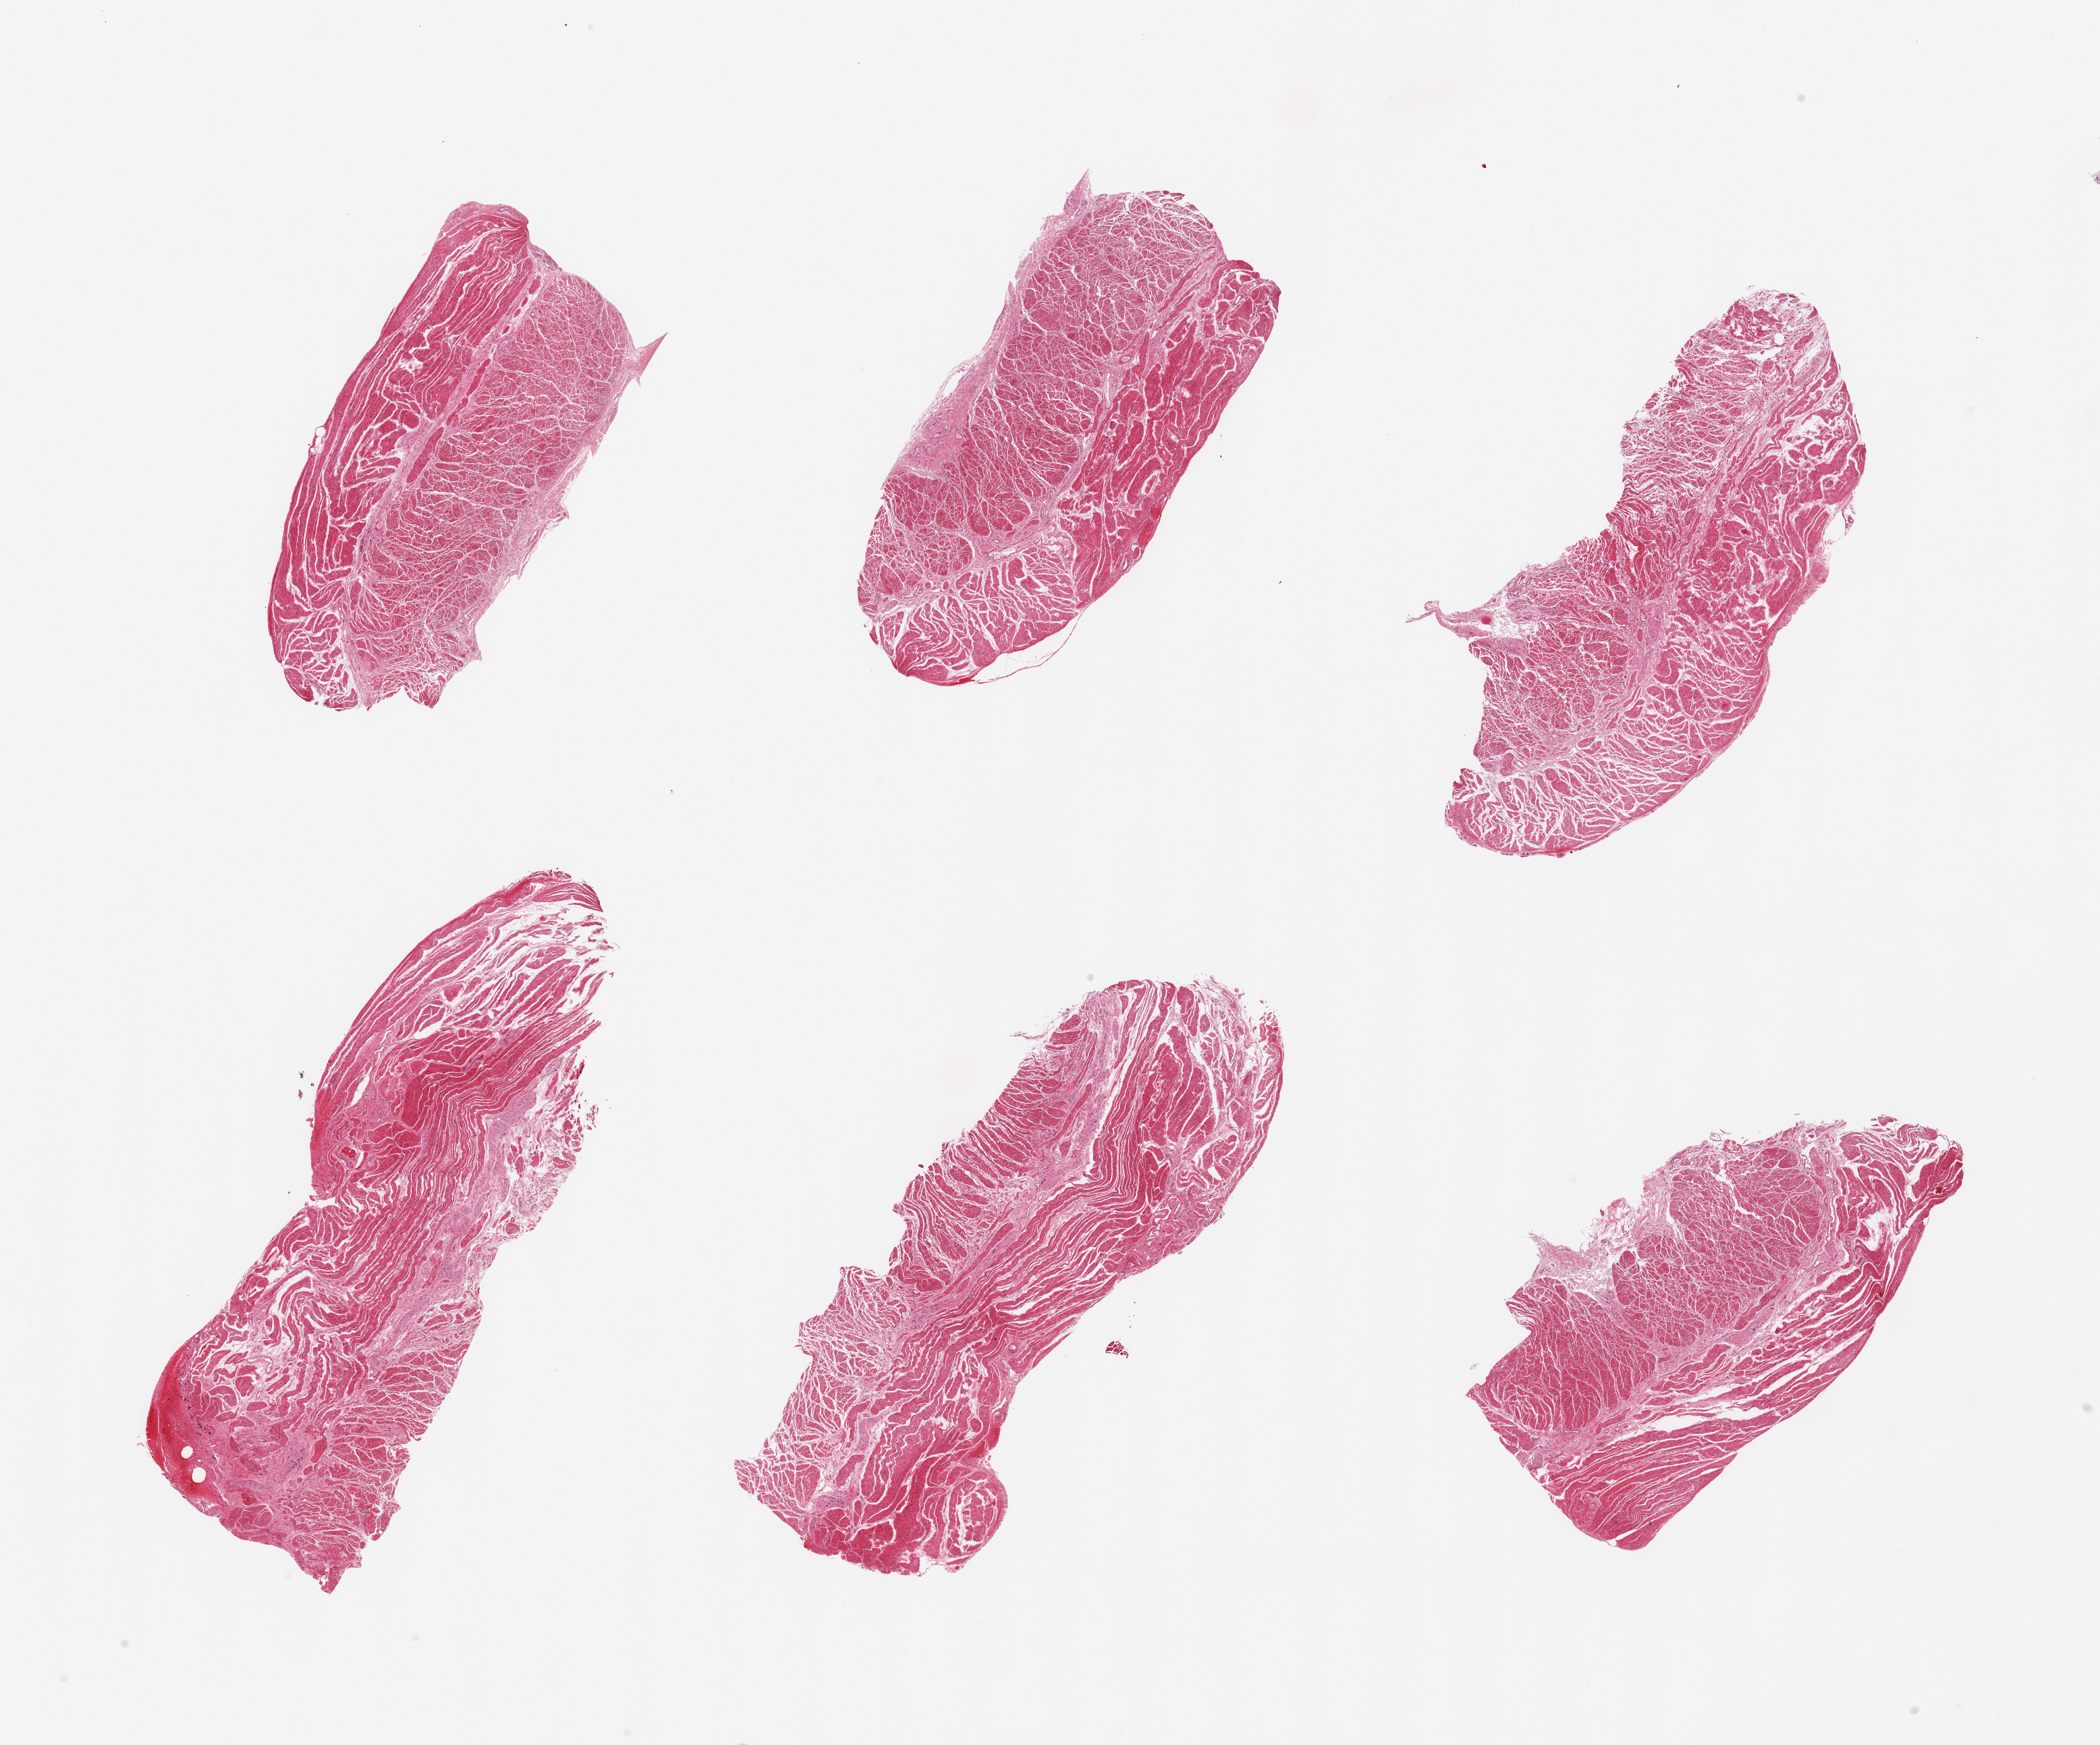
H&E whole-slide image, whole scanned area (about 24.6 x 20.5 mm, slide scanned at 20x) shown as a low-resolution overview. PAXgene-fixed paraffin-embedded (PFPE) section. Section of esophageal muscle (target tissue). Tissue donor sample. Donor sex: female.
Reviewer comment on this tissue sample: 6 pieces; target musculairs.